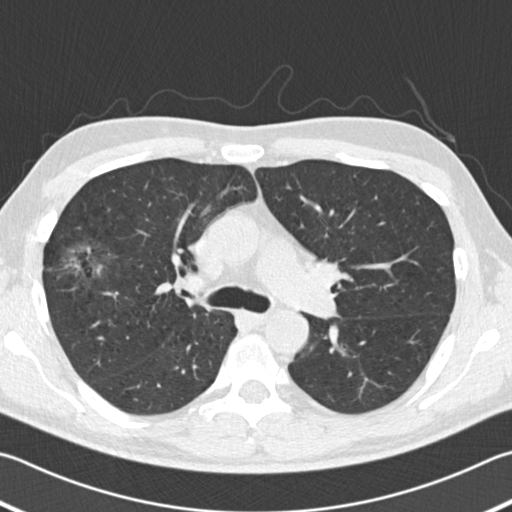
Low-dose screening chest CT, one axial slice. Slice 119 of 182 in the series (ordered by position). Reconstruction kernel B30f. 120 kVp. Lung window (W 1500 / L -600 HU). 2 mm slice thickness. 512 × 512 image matrix, field of view 344 × 344 mm.
Outlined on this slice (outlined manually by an expert reader):
- lesion 1 (tumor, upper lobe of right lung): bounding box (x1, y1, x2, y2) in pixels: (64, 242, 107, 281)